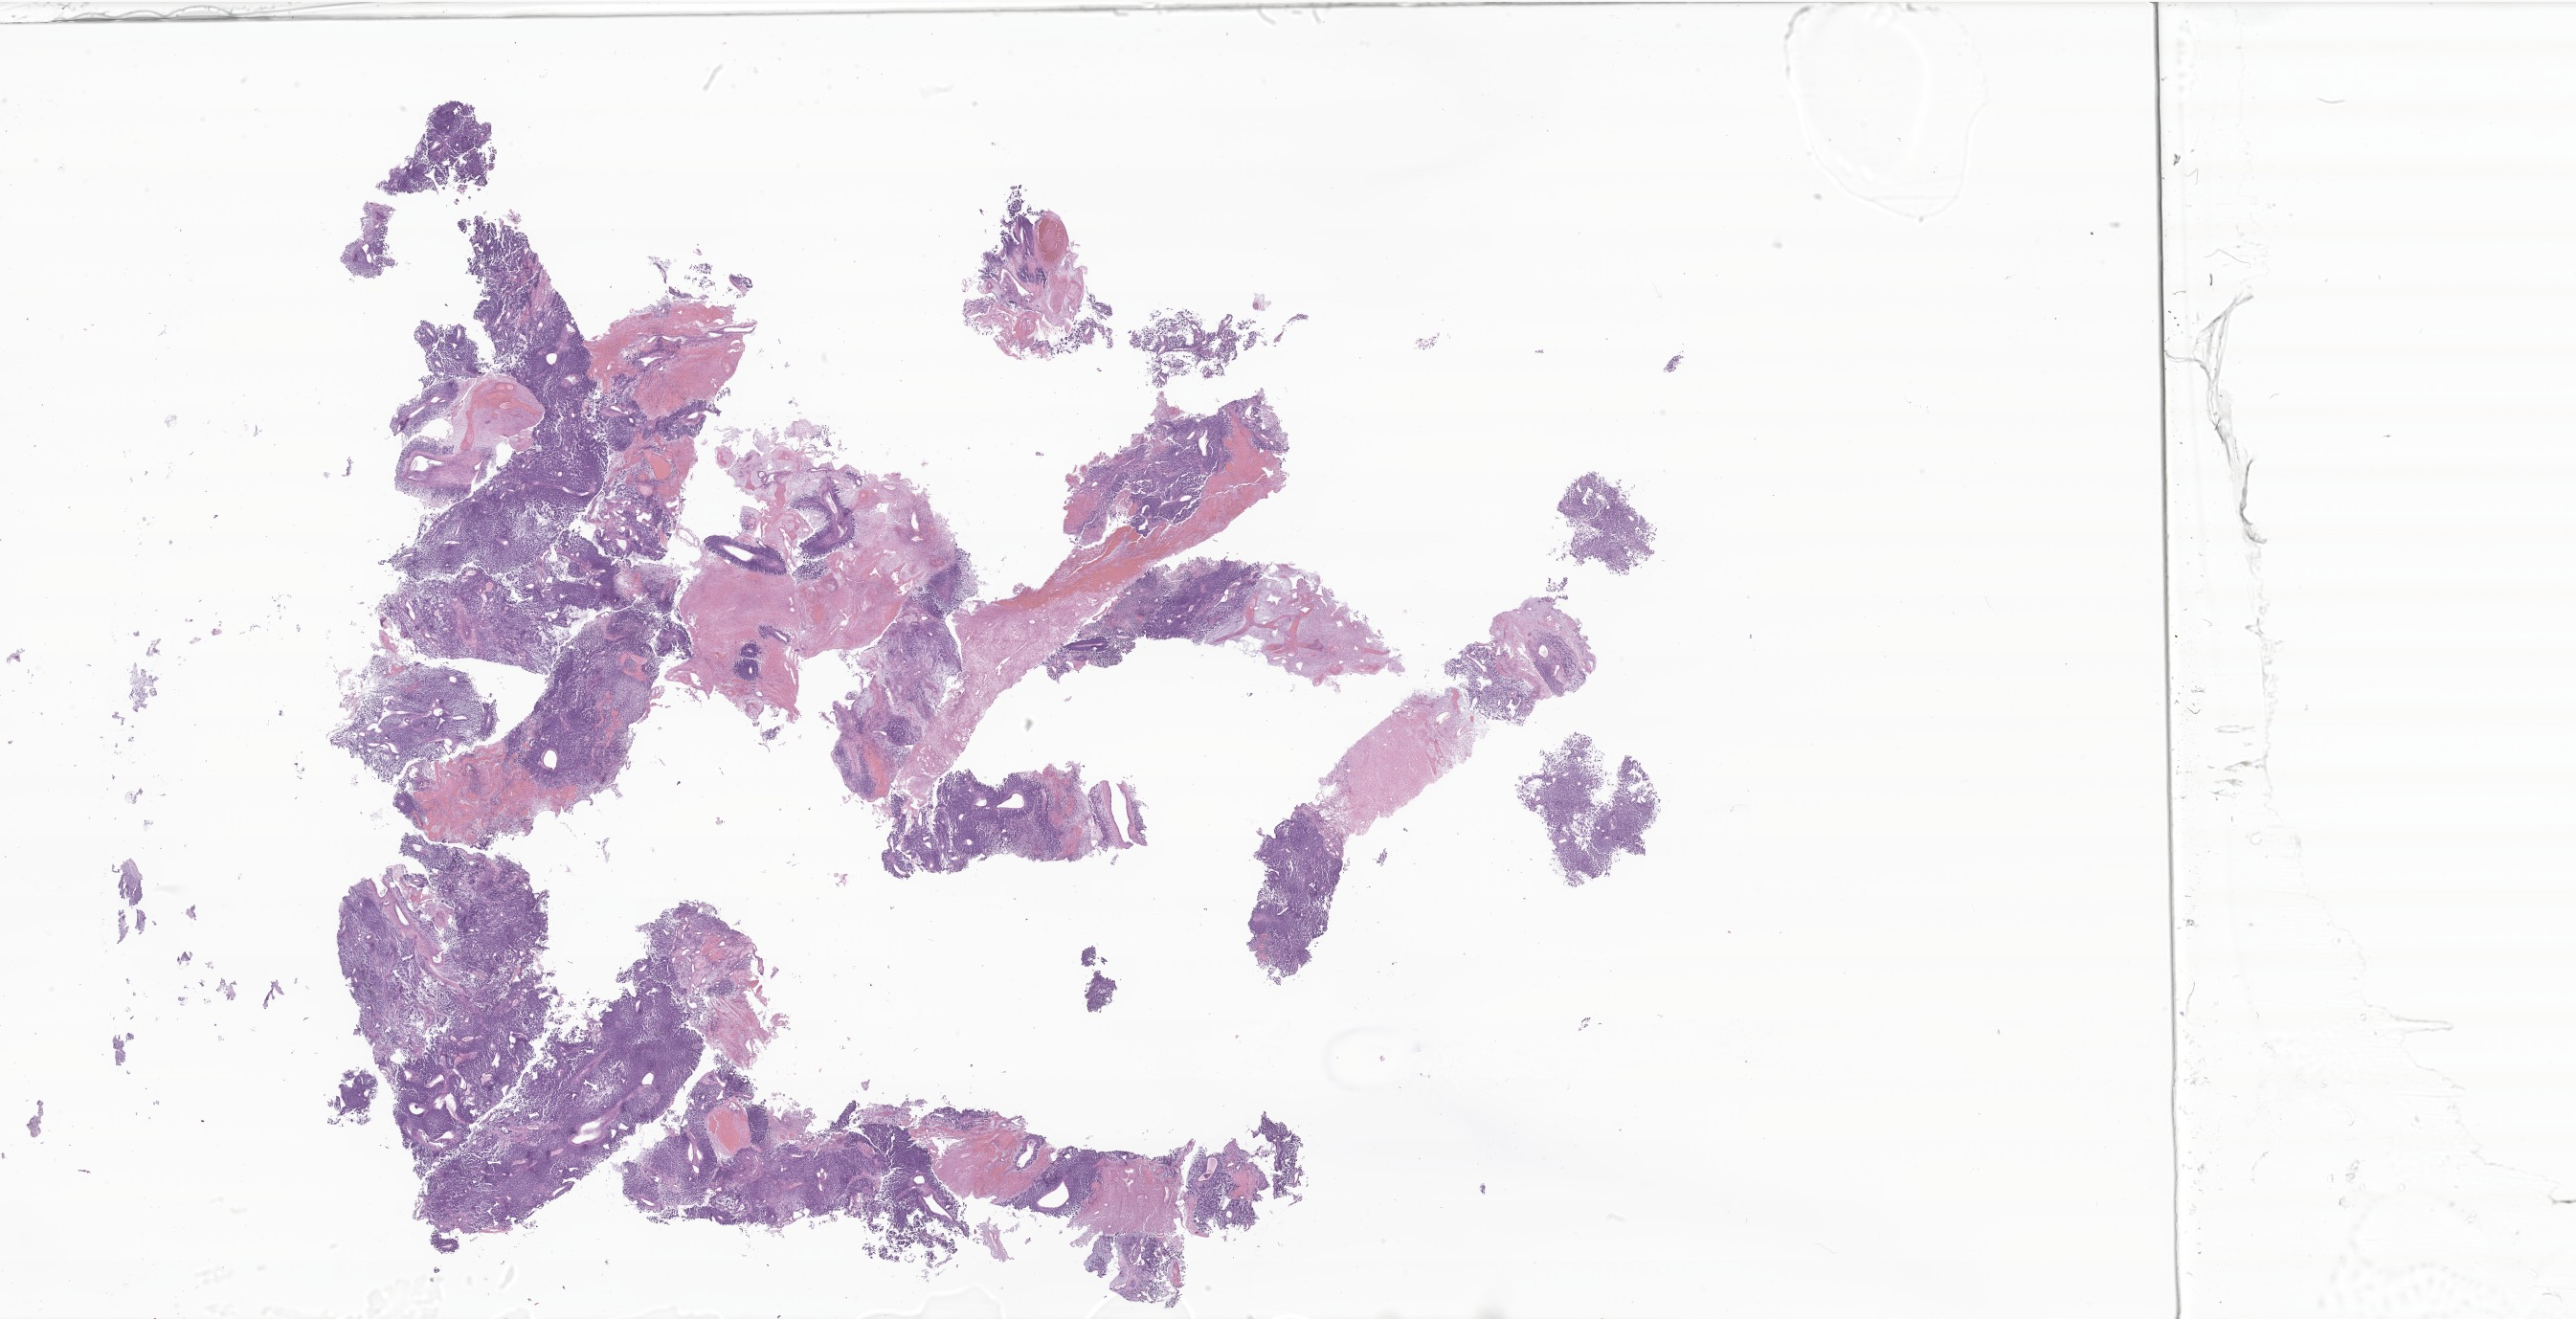
Whole-slide image, H&E stain of tumor tissue from the soft tissue of abdomen, a low-resolution overview of the entire scanned area, about 45.4 x 23.2 mm, formalin-fixed, paraffin-embedded (FFPE) tissue. Patient: male, age 304 months.
Diagnosis (ICD-O-3 morphology term): Myxoid chondrosarcoma. Tissue or organ of origin (case record): connective, subcutaneous and other soft tissues of abdomen.